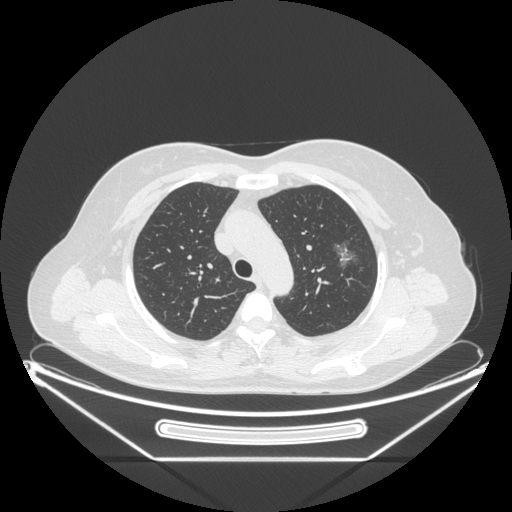
Chest CT, one axial slice. Position 162 of 226 along the scan axis. 120 kVp. Lung window (W 1500 / L -600 HU). 1.25 mm slice thickness. 512 × 512 image matrix. Female patient, age 54 years. From the clinical record (not read from this slice): clinical TNM (as recorded): T1c N0 M0.
Outlined on this slice (bounding box drawn by a radiologist):
- lung tumour (recorded histology: adenocarcinoma): bounding box <330,238,364,276> (left, top, right, bottom; pixels)